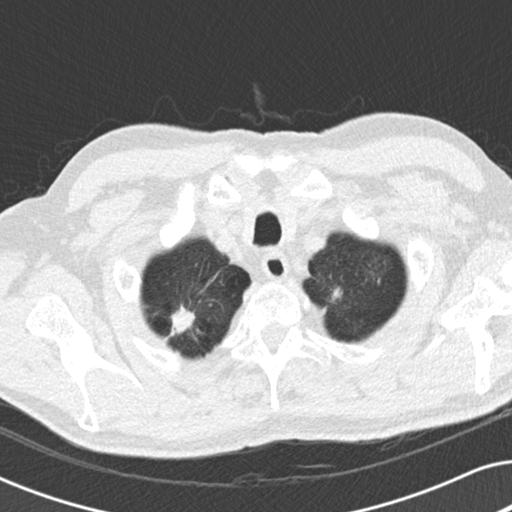
Low-dose screening chest CT, one axial slice. Position 173 of 191 along the scan axis. 120 kVp. Lung window (W 1500 / L -600 HU). 2 mm slice thickness. 512 × 512 image matrix, field of view 330 × 330 mm.
Outlined on this slice (expert manual segmentation):
- lesion 2 (nodule, lower lobe of right lung): bounding box [x1, y1, x2, y2] px = [168, 306, 195, 337]